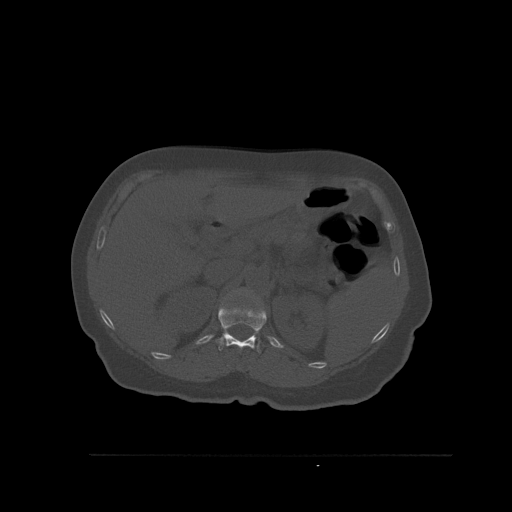
CT including the spine, one axial slice; position 283 of 527 along the scan axis; bone window (W 1800 / L 400 HU); 1.5 mm slice thickness; 512 × 512 image matrix, field of view 470 × 470 mm. Female patient, age 73 years. Case-level facts recorded for this patient, not image findings: primary cancer: breast.
Annotated regions visible in this slice (semi-automatically segmented with operator editing):
- L1 vertebra: bounding box (x1, y1, x2, y2) in pixels: (246, 290, 248, 295)
- T12 vertebra: (216, 305, 267, 353)